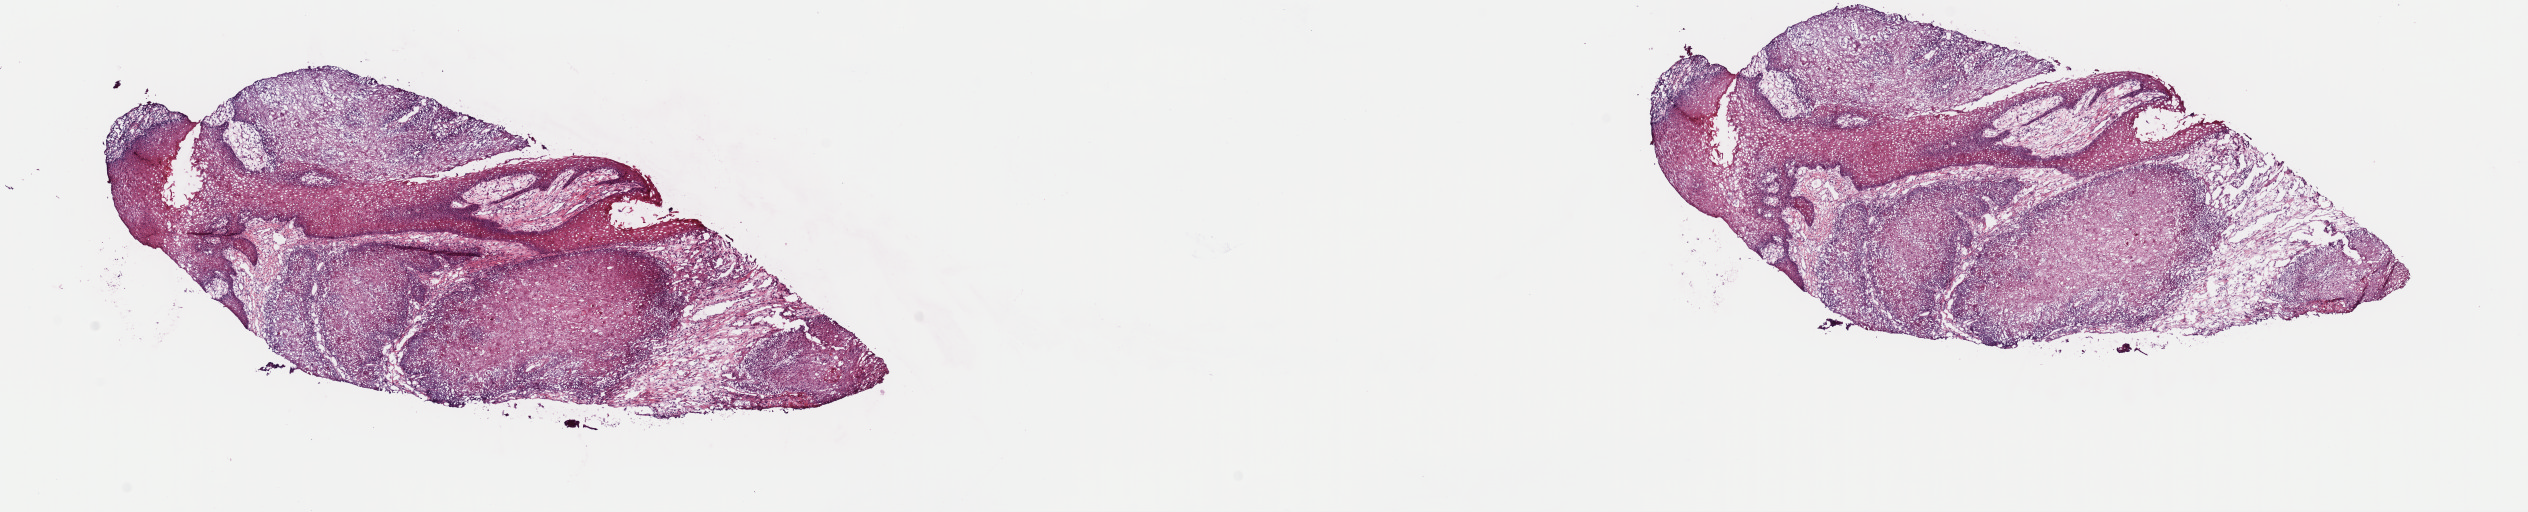
H&E-stained whole-slide image, whole scanned area (about 20.0 x 4.0 mm, from a 40x scan) shown as a low-resolution overview. Frozen section from the top of the tissue portion. Sample: primary tumour, head and neck. Patient: male, age at initial diagnosis 69 years. Histologic grade: G2 (moderately differentiated). Composition of this section per pathologist review: tumour cells 70%, tumour nuclei 90%, normal cells 0%, stromal cells 30%, necrosis 0%. Inflammatory infiltration, as recorded: lymphocyte infiltration 0%, monocyte infiltration 0%, neutrophil infiltration 0%.
- AJCC pathologic stage: IVA (7th edition)
- lymph nodes positive (case pathology): 10 of 51 examined
- diagnosis: Squamous cell carcinoma, NOS (tongue, NOS)